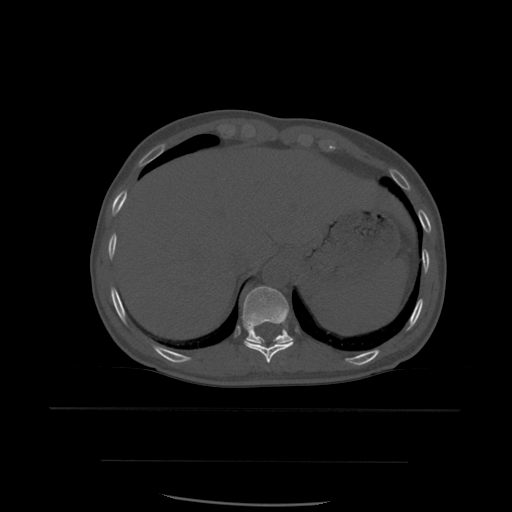
CT including the spine, one axial slice. Position 307 of 574 along the scan axis. Bone window (W 1800 / L 400 HU). 1.25 mm slice thickness. 512 × 512 image matrix, field of view 392 × 392 mm. Patient age 48 years. From the clinical record (not read from this slice): primary cancer: lung.
Annotated regions visible in this slice (semi-automatically segmented with operator editing):
- T10 vertebra: bounding box (x1, y1, x2, y2) in pixels: (244, 341, 294, 363)
- T11 vertebra: (242, 286, 294, 346)